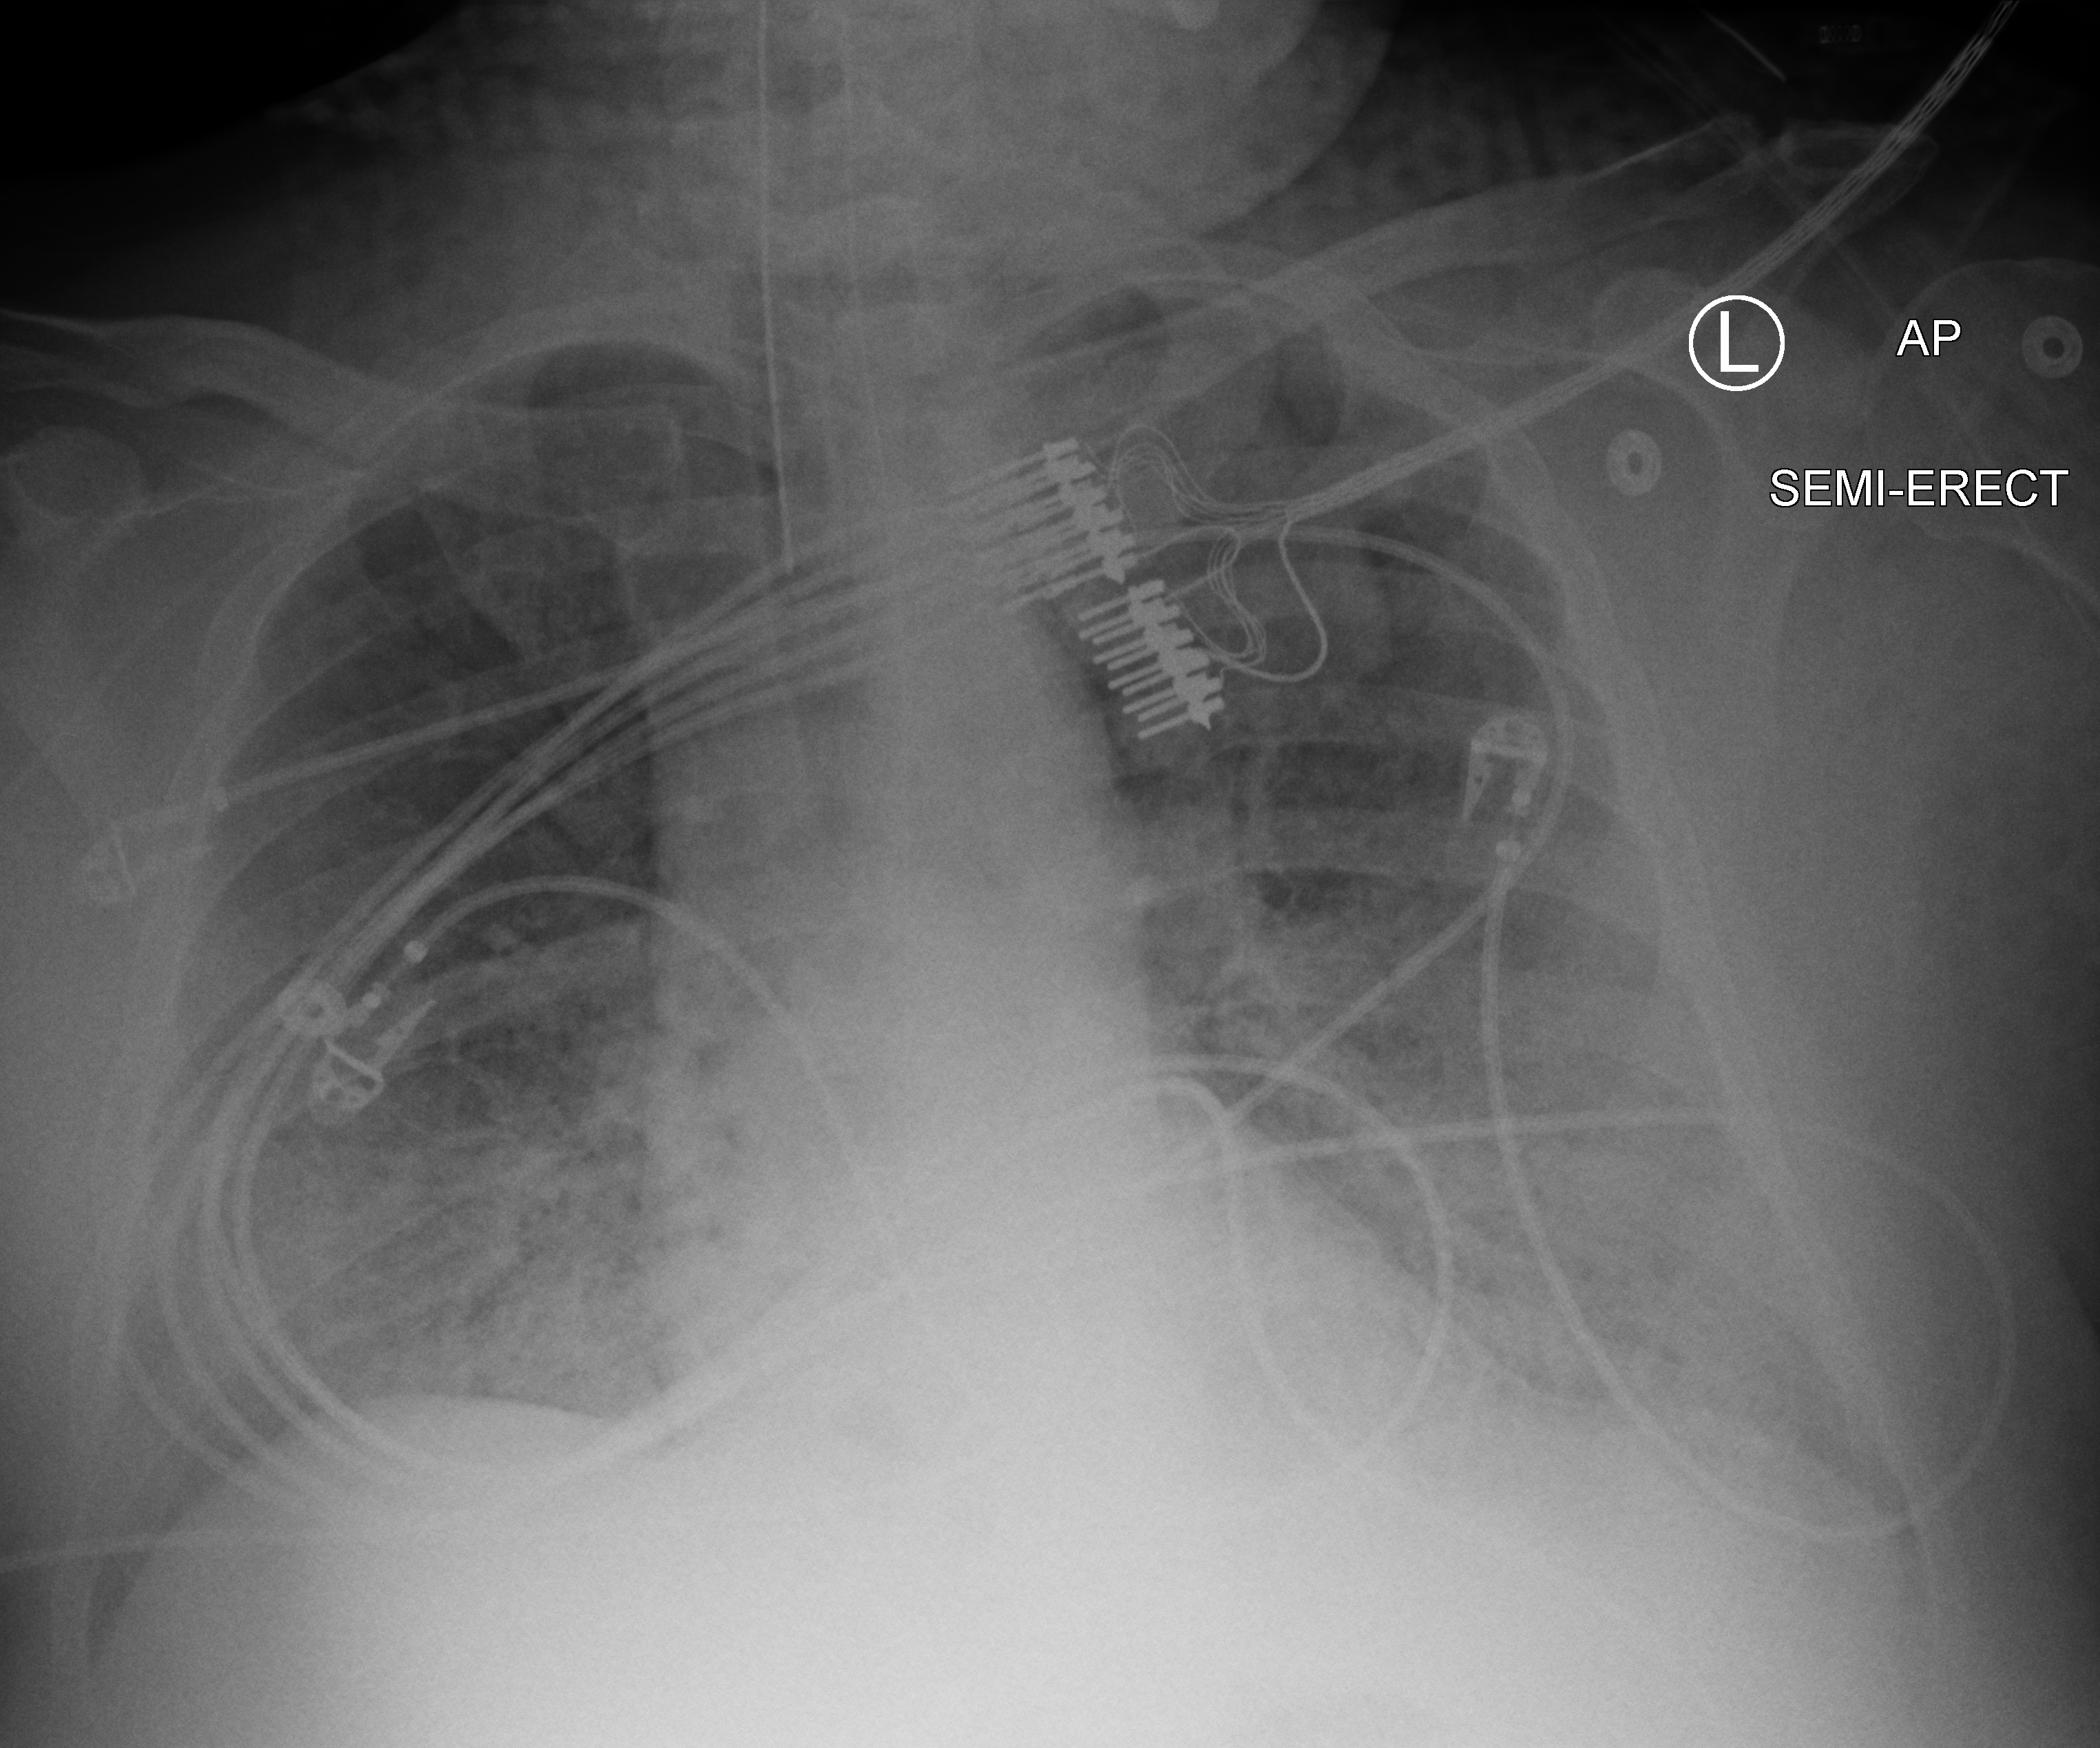
Chest X-ray (portable). Patient hospitalised with COVID-19, aged 18–59 years.
From the hospital-stay record, not from the radiograph (when in the stay this image was taken is not recorded): mechanically ventilated during this hospital stay: yes; smoking status (admission record): never.